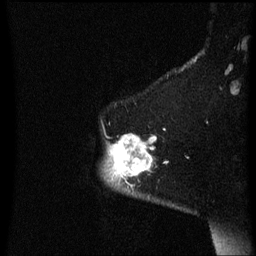
Breast MRI (dynamic contrast-enhanced), one sagittal slice. Slice 52 of 60 in the series (ordered by position). Dynamic contrast-enhanced series, image 2 of 3 at this slice position (ordered by acquisition). 1.5 T. TE 4.2 ms, TR 8.4 ms. 2 mm slice thickness. 256 × 256 image matrix. Patient: female, 54 years. Case-level facts recorded for this patient, not image findings: setting: breast cancer imaged before/during neoadjuvant chemotherapy; receptor status: HR-positive, HER2-negative.
Annotated regions visible in this slice (semi-automatically segmented with operator editing):
- analysis volume of interest (the breast-tissue region the enhancement analysis was run in; not a lesion): bounding box <102,134,158,191> (left, top, right, bottom; pixels)
- tumour enhancement mask (voxels above the 70 % enhancement threshold inside the analysis volume of interest): <109,134,158,183>